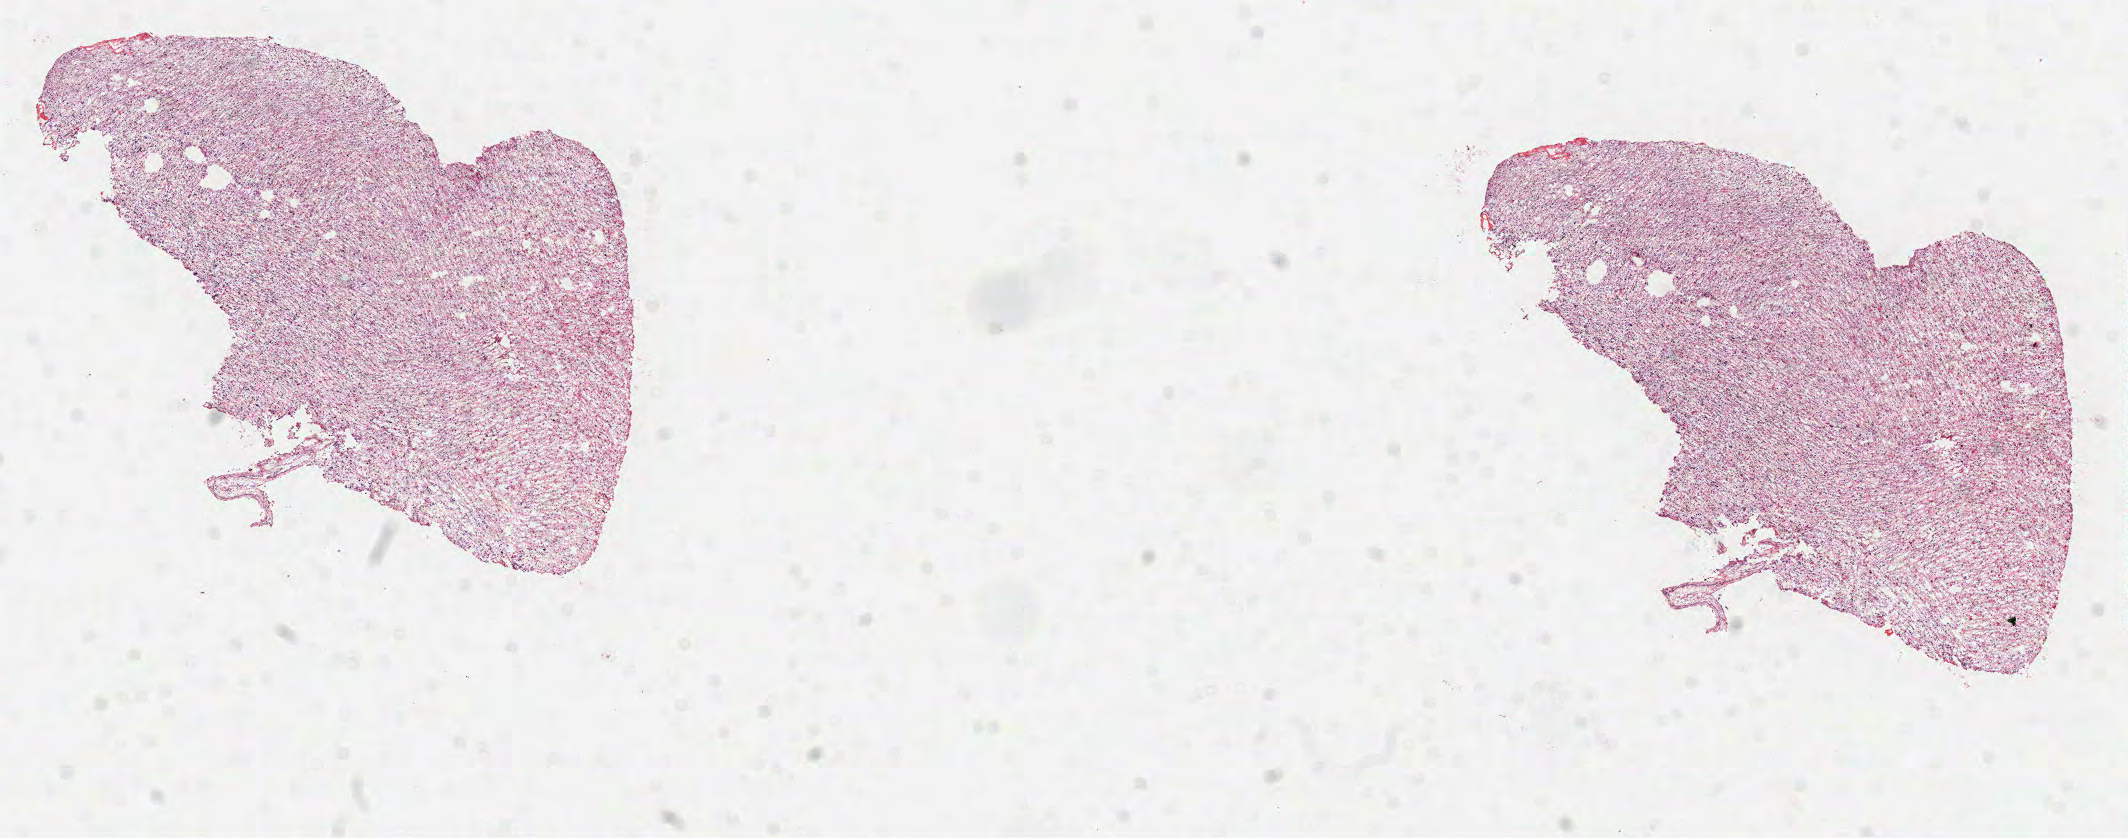
Whole-slide histology image, Hematoxylin and eosin (H&E) stained, low-resolution overview of the scanned area, about 17.2 x 6.8 mm, FFPE section, primary tumour sample from the brain. Male, age 60 years at initial diagnosis.
Histologic diagnosis: Glioblastoma.